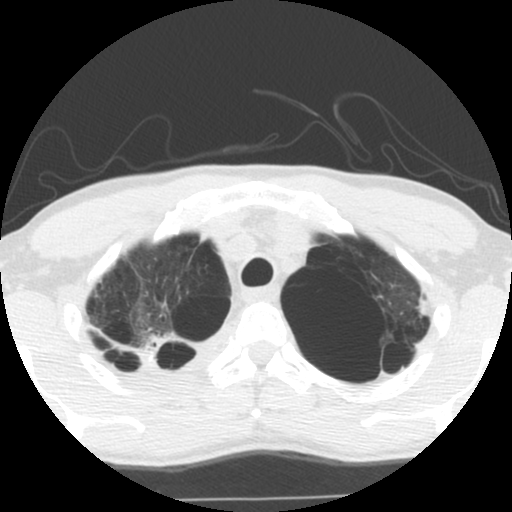
Low-dose screening chest CT, one axial slice; slice 98 of 119 in the series (ordered by position); reconstruction kernel STANDARD; 140 kVp; lung window (W 1500 / L -600 HU); 2.5 mm slice thickness; 512 × 512 image matrix, field of view 295 × 295 mm.
Annotated regions visible in this slice (outlined manually by an expert reader):
- lesion 1 (tumor, upper lobe of right lung): bounding box (x1, y1, x2, y2) in pixels: (137, 331, 173, 368)